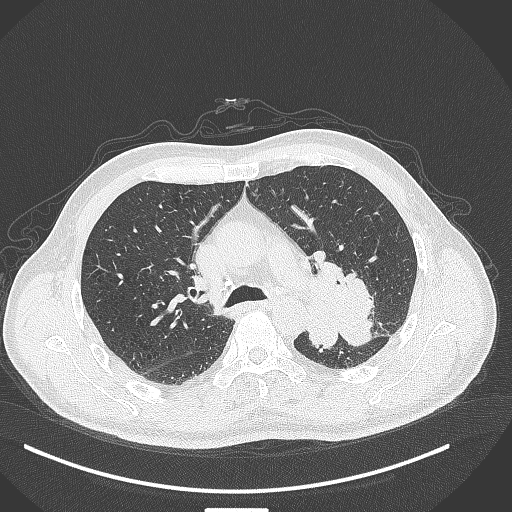
Chest CT, one axial slice; position 278 of 429 along the scan axis; lung window (W 1500 / L -600 HU); 512 × 512 image matrix, field of view 400 × 400 mm. Male patient, age 55 years. Case-level facts recorded for this patient, not image findings: clinical TNM (as recorded): T3 N0 M1c.
Outlined on this slice (rectangle marked by the reading radiologist):
- lung tumour (recorded histology: adenocarcinoma): bounding box (x1, y1, x2, y2) in pixels: (312, 256, 380, 353)